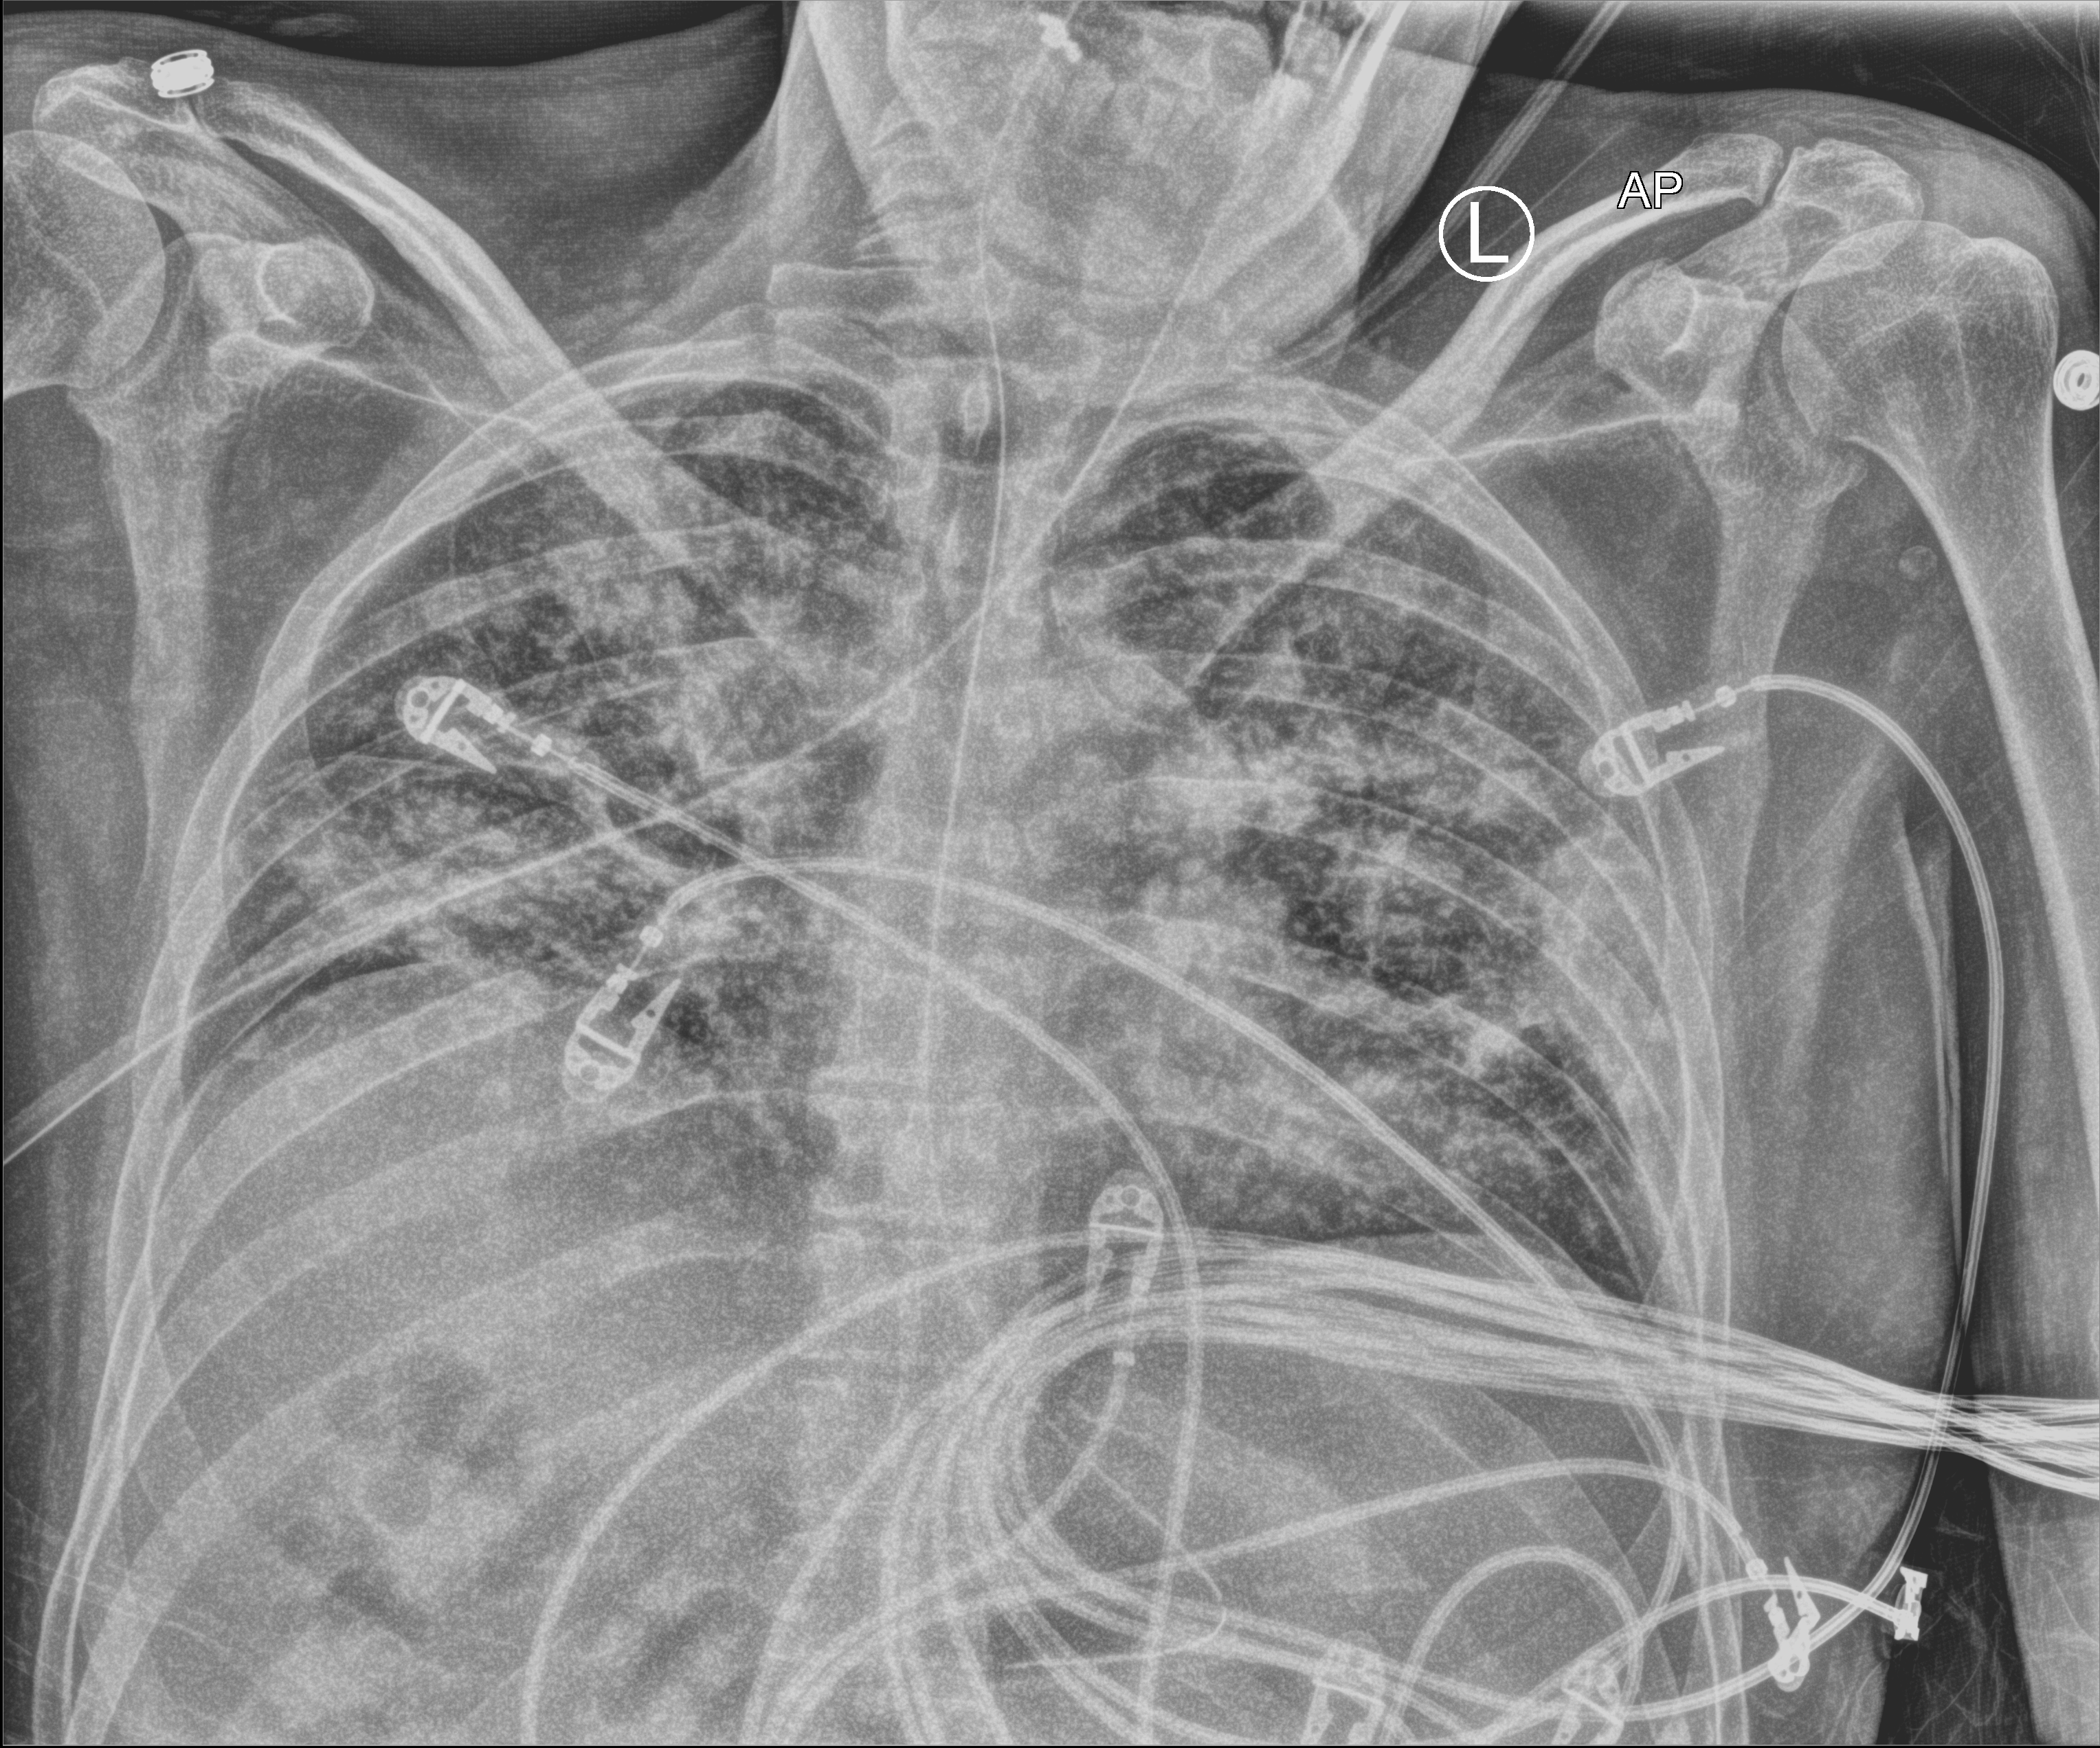
Chest X-ray (portable); anteroposterior (AP) projection. Male patient hospitalised with COVID-19, age 18–59 years.
From the hospital-stay record, not from the radiograph (when in the stay this image was taken is not recorded): length of hospital stay: 48 days; hypertension (admission record): no.